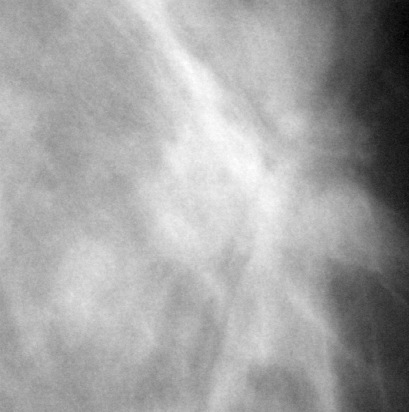
Crop from a digitized film mammogram around one marked abnormality; left breast; MLO view; BI-RADS breast density category 2 (scale 1–4).
Marked abnormality: mass, shape irregular, margins spiculated; BI-RADS assessment category 5; pathology result (as recorded, not read from the image): malignant.